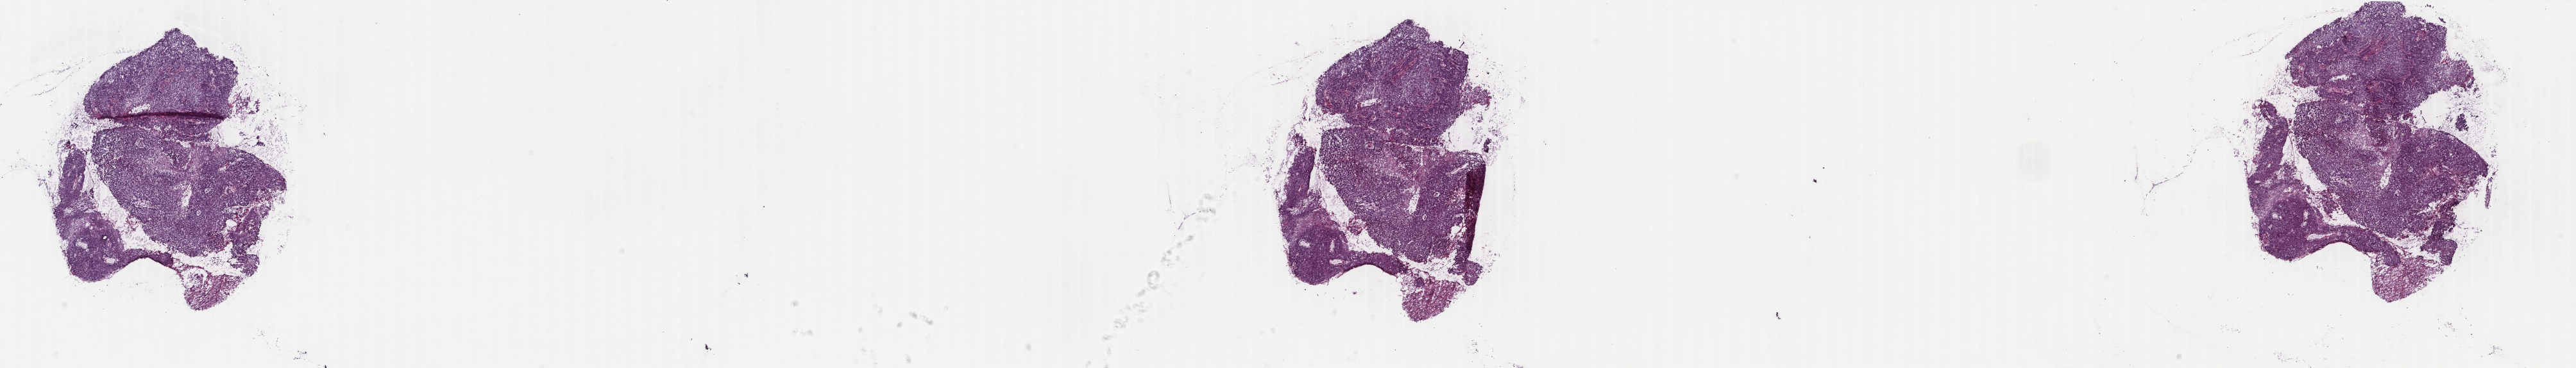
Whole-slide histology image, H&E-stained, shown as a low-resolution overview of the whole scanned area (about 31.9 x 4.6 mm). Frozen section. Lung, primary tumour sample. Male, age 68 years at initial diagnosis. Composition of this section per pathologist review: tumour cells 85%, tumour nuclei 90%, normal cells 0%, stromal cells 14%, necrosis 1%. Inflammatory infiltration, as recorded: lymphocyte infiltration 0%, monocyte infiltration 0%, neutrophil infiltration 0%.
• AJCC pathologic stage: IA
• laterality: left
• histologic diagnosis: Squamous cell carcinoma, NOS (lower lobe, lung)